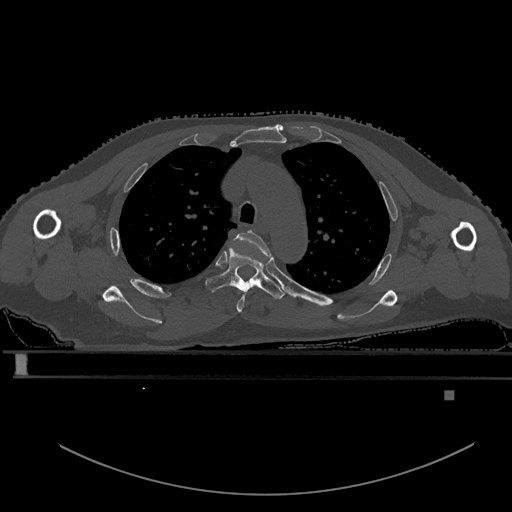
CT including the spine, one axial slice; position 419 of 969 along the scan axis; bone window (W 1800 / L 400 HU); 512 × 512 image matrix, field of view 456 × 456 mm. Male patient, age 82 years. From the clinical record (not read from this slice): primary cancer: prostate; vertebrae with lytic lesions (as recorded): T11, T9, T8, T2.
Outlined on this slice (semi-automatically segmented with operator editing):
- T3 vertebra: box from (x=235, y=230) to (x=271, y=313) px
- T4 vertebra: (x=206, y=247)–(x=285, y=299)